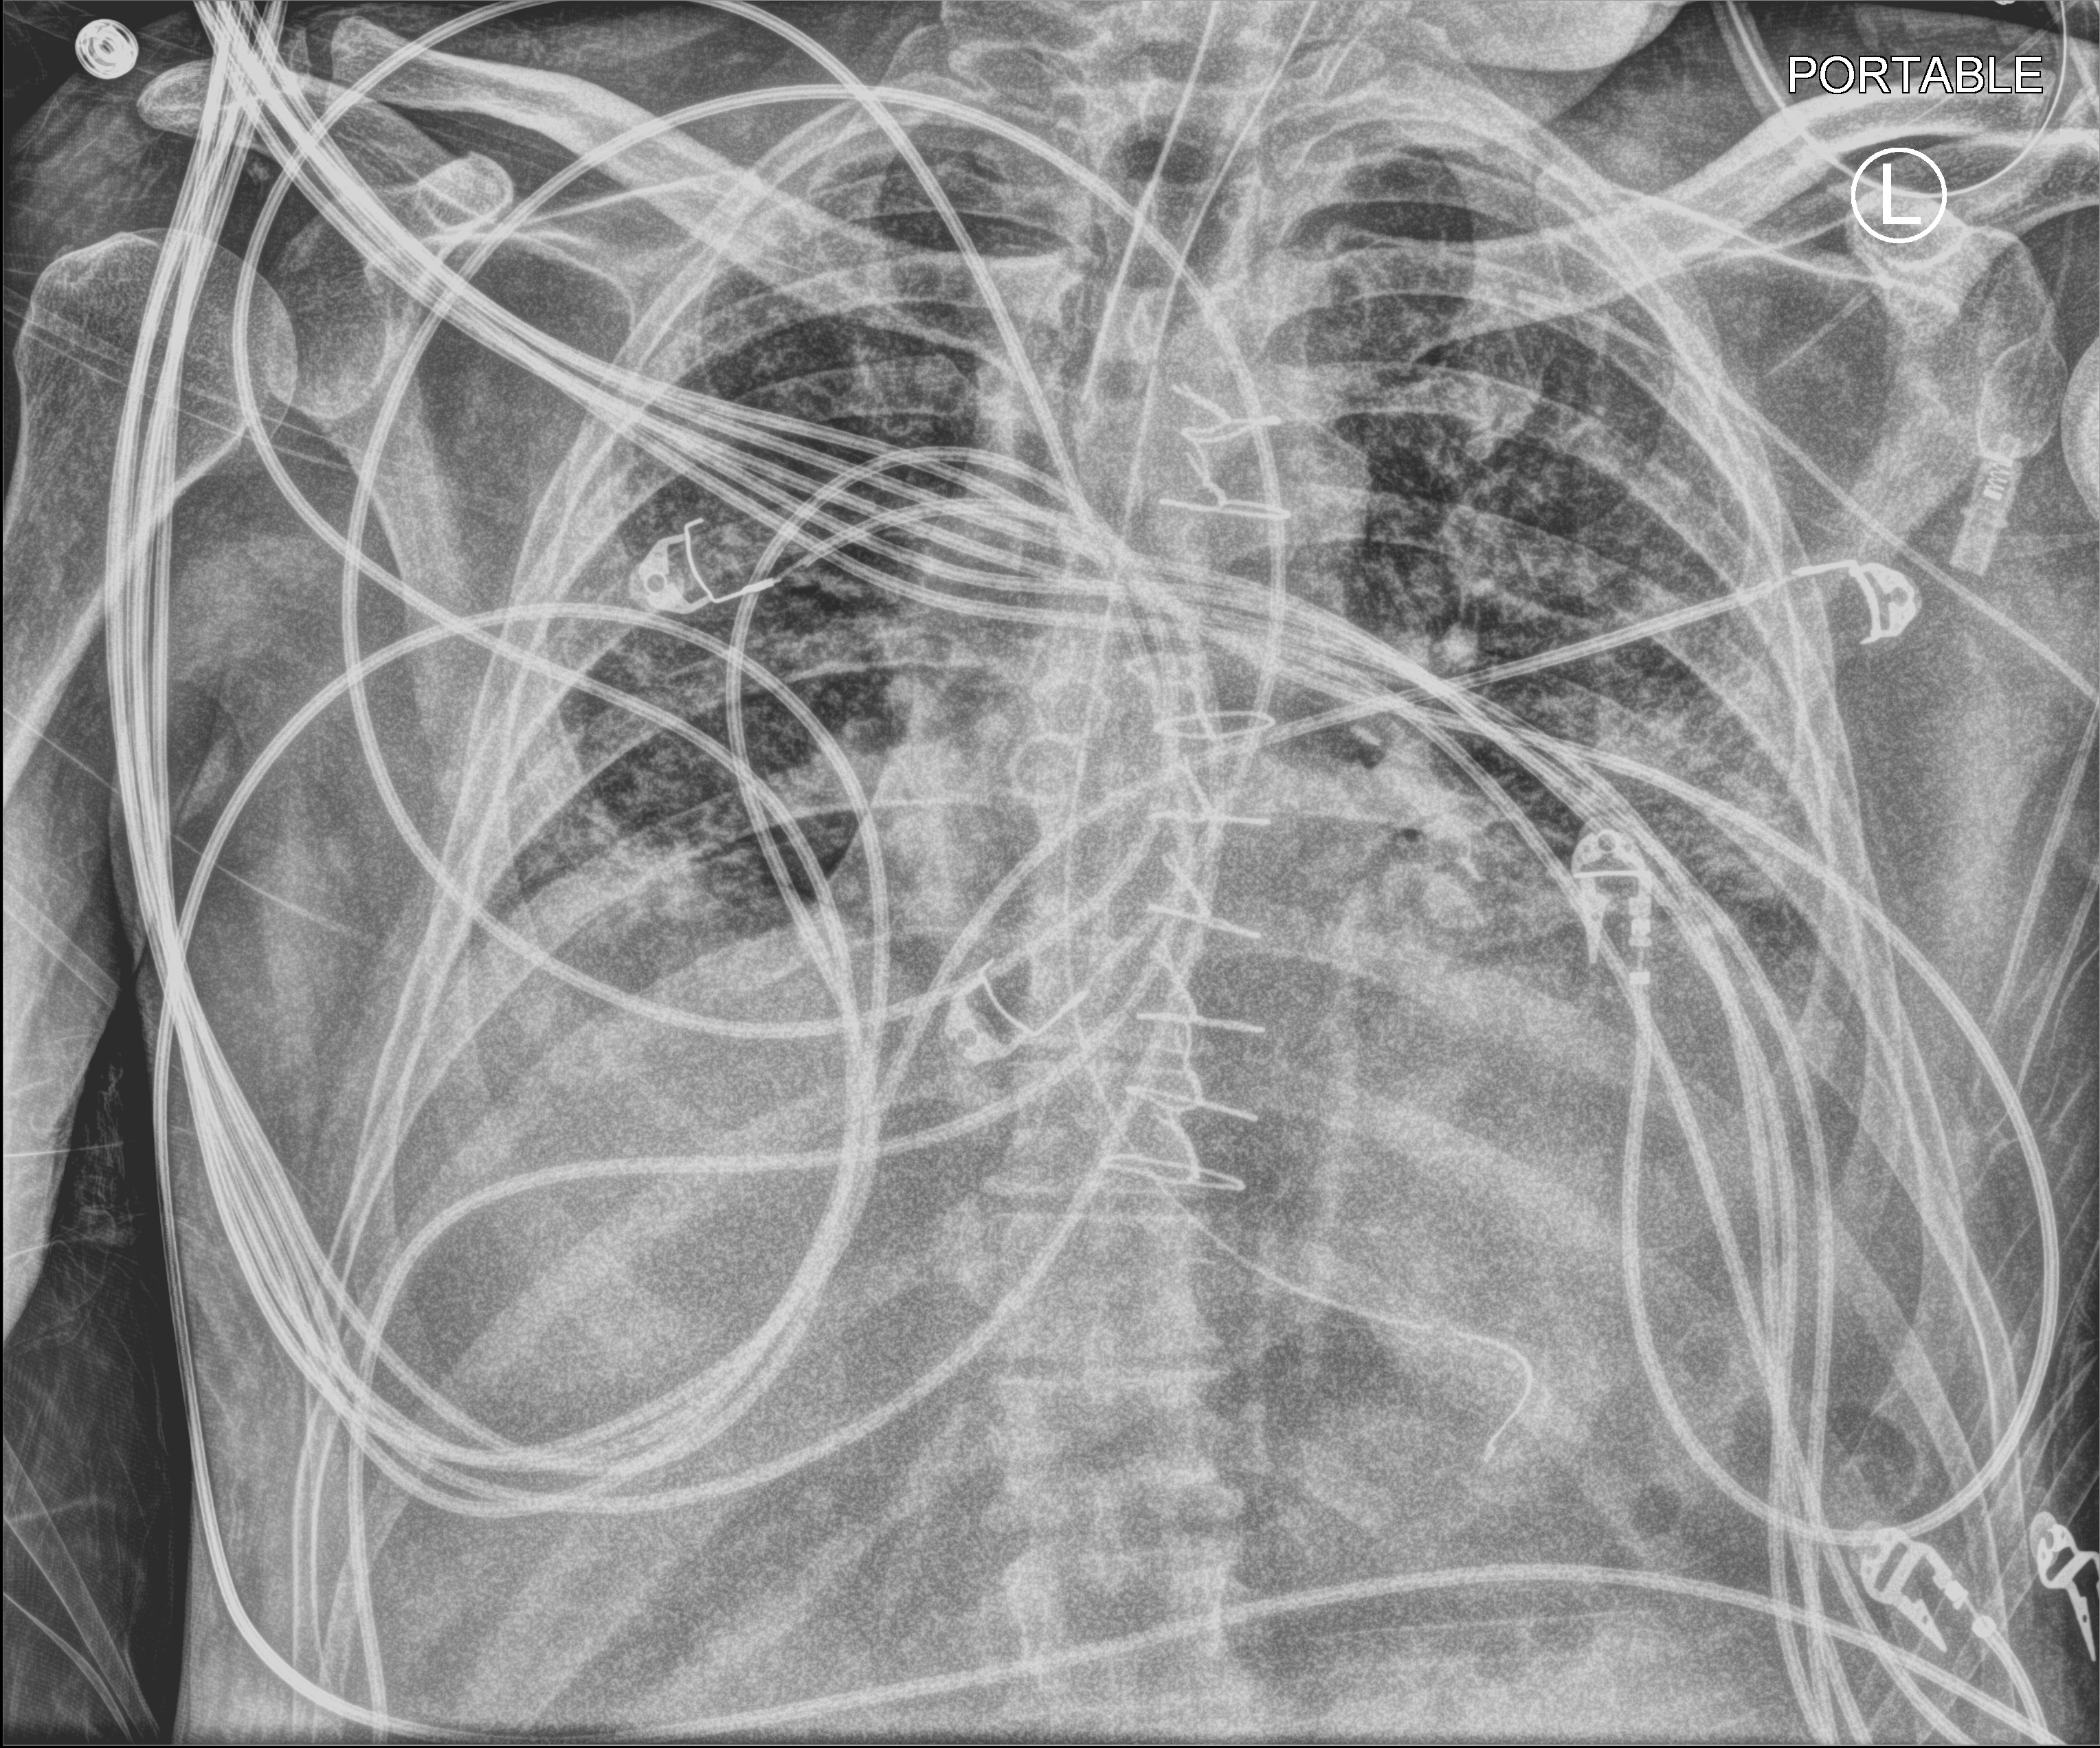
Bedside chest radiograph (computed radiography), anteroposterior (AP) projection. Male patient hospitalised with COVID-19, age 18–59 years.
From the hospital-stay record, not from the radiograph (when in the stay this image was taken is not recorded): mechanically ventilated during this hospital stay: yes; admitted to intensive care during this hospital stay: yes.